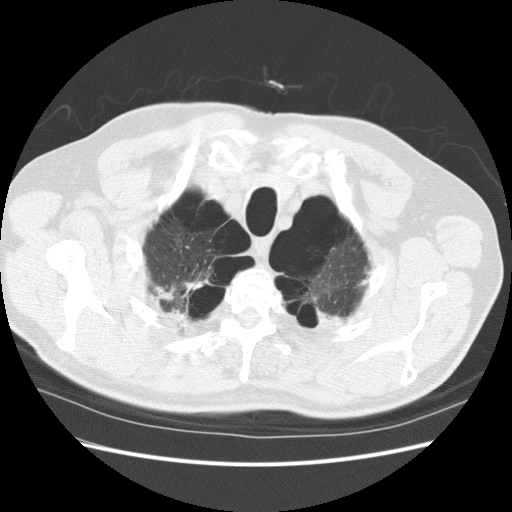
Chest CT (low-dose screening protocol), one axial image, first (baseline) screen, lung window (W 1500 / L -600 HU). Male, age 68 years at enrolment. Former smoker at enrolment.
- Expert reader's lesion annotation, bounding box [x1, y1, x2, y2] px = [138, 264, 217, 329].
- The screening reader recorded 2 non-calcified nodules or masses ≥4 mm on this exam (left lower lobe, lingula); which of them this box marks is not recorded.
- Official screen result: positive, change unspecified: nodule(s) >= 4 mm or enlarging nodule(s), mass(es), or other non-specific abnormalities suspicious for lung cancer.
- Later outcome: lung cancer diagnosed 1003 days after this screen (after the third annual screen) — large cell carcinoma, NOS, right upper lobe, poorly differentiated (G3), stage IV (AJCC 6th edition).